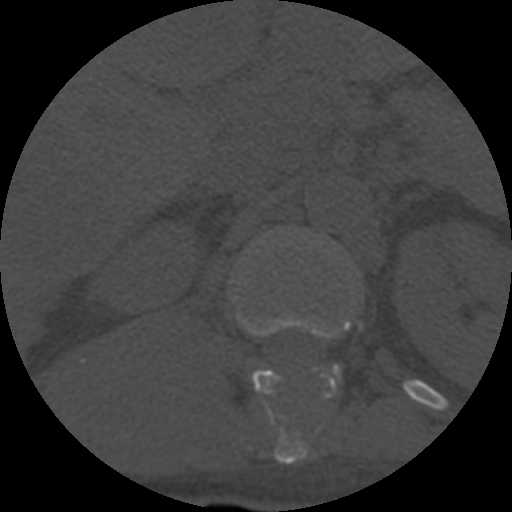
CT including the spine, one axial slice. Position 303 of 708 along the scan axis. Reconstruction kernel STANDARD. 120 kVp. One of 3 acquisitions stored at this slice position. Bone window (W 1800 / L 400 HU). 1.25 mm slice thickness. 512 × 512 image matrix, field of view 160 × 160 mm. Patient age 55 years. Case-level facts recorded for this patient, not image findings: primary cancer: colon; vertebrae with lytic lesions (as recorded): T12, L1, L5.
Structures marked on this image (semi-automatically segmented with operator editing):
- L1 vertebra: bounding box (x1, y1, x2, y2) in pixels: (327, 367, 340, 397)
- T12 vertebra: (240, 315, 362, 464)